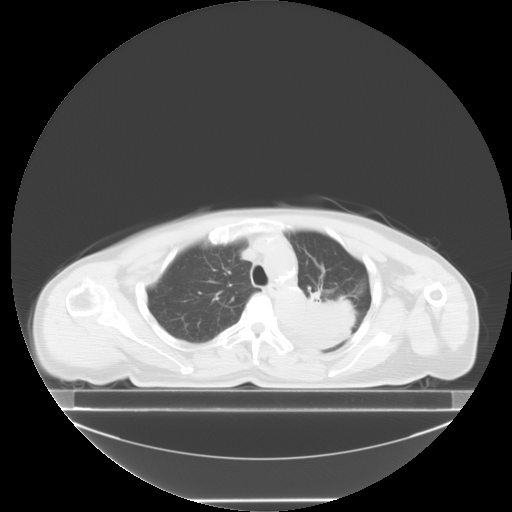
Chest CT, one axial slice. Position 10 of 24 along the scan axis. Reconstruction kernel STANDARD. 120 kVp. Lung window (W 1500 / L -600 HU). 5 mm slice thickness. 512 × 512 image matrix. Female patient, age 74 years. Case-level facts recorded for this patient, not image findings: clinical TNM (as recorded): T3 N1 M1c; histopathological grade: G3.
Annotated regions visible in this slice (bounding box drawn by a radiologist):
- lung tumour (recorded histology: small cell carcinoma): box from (x=295, y=289) to (x=363, y=356) px